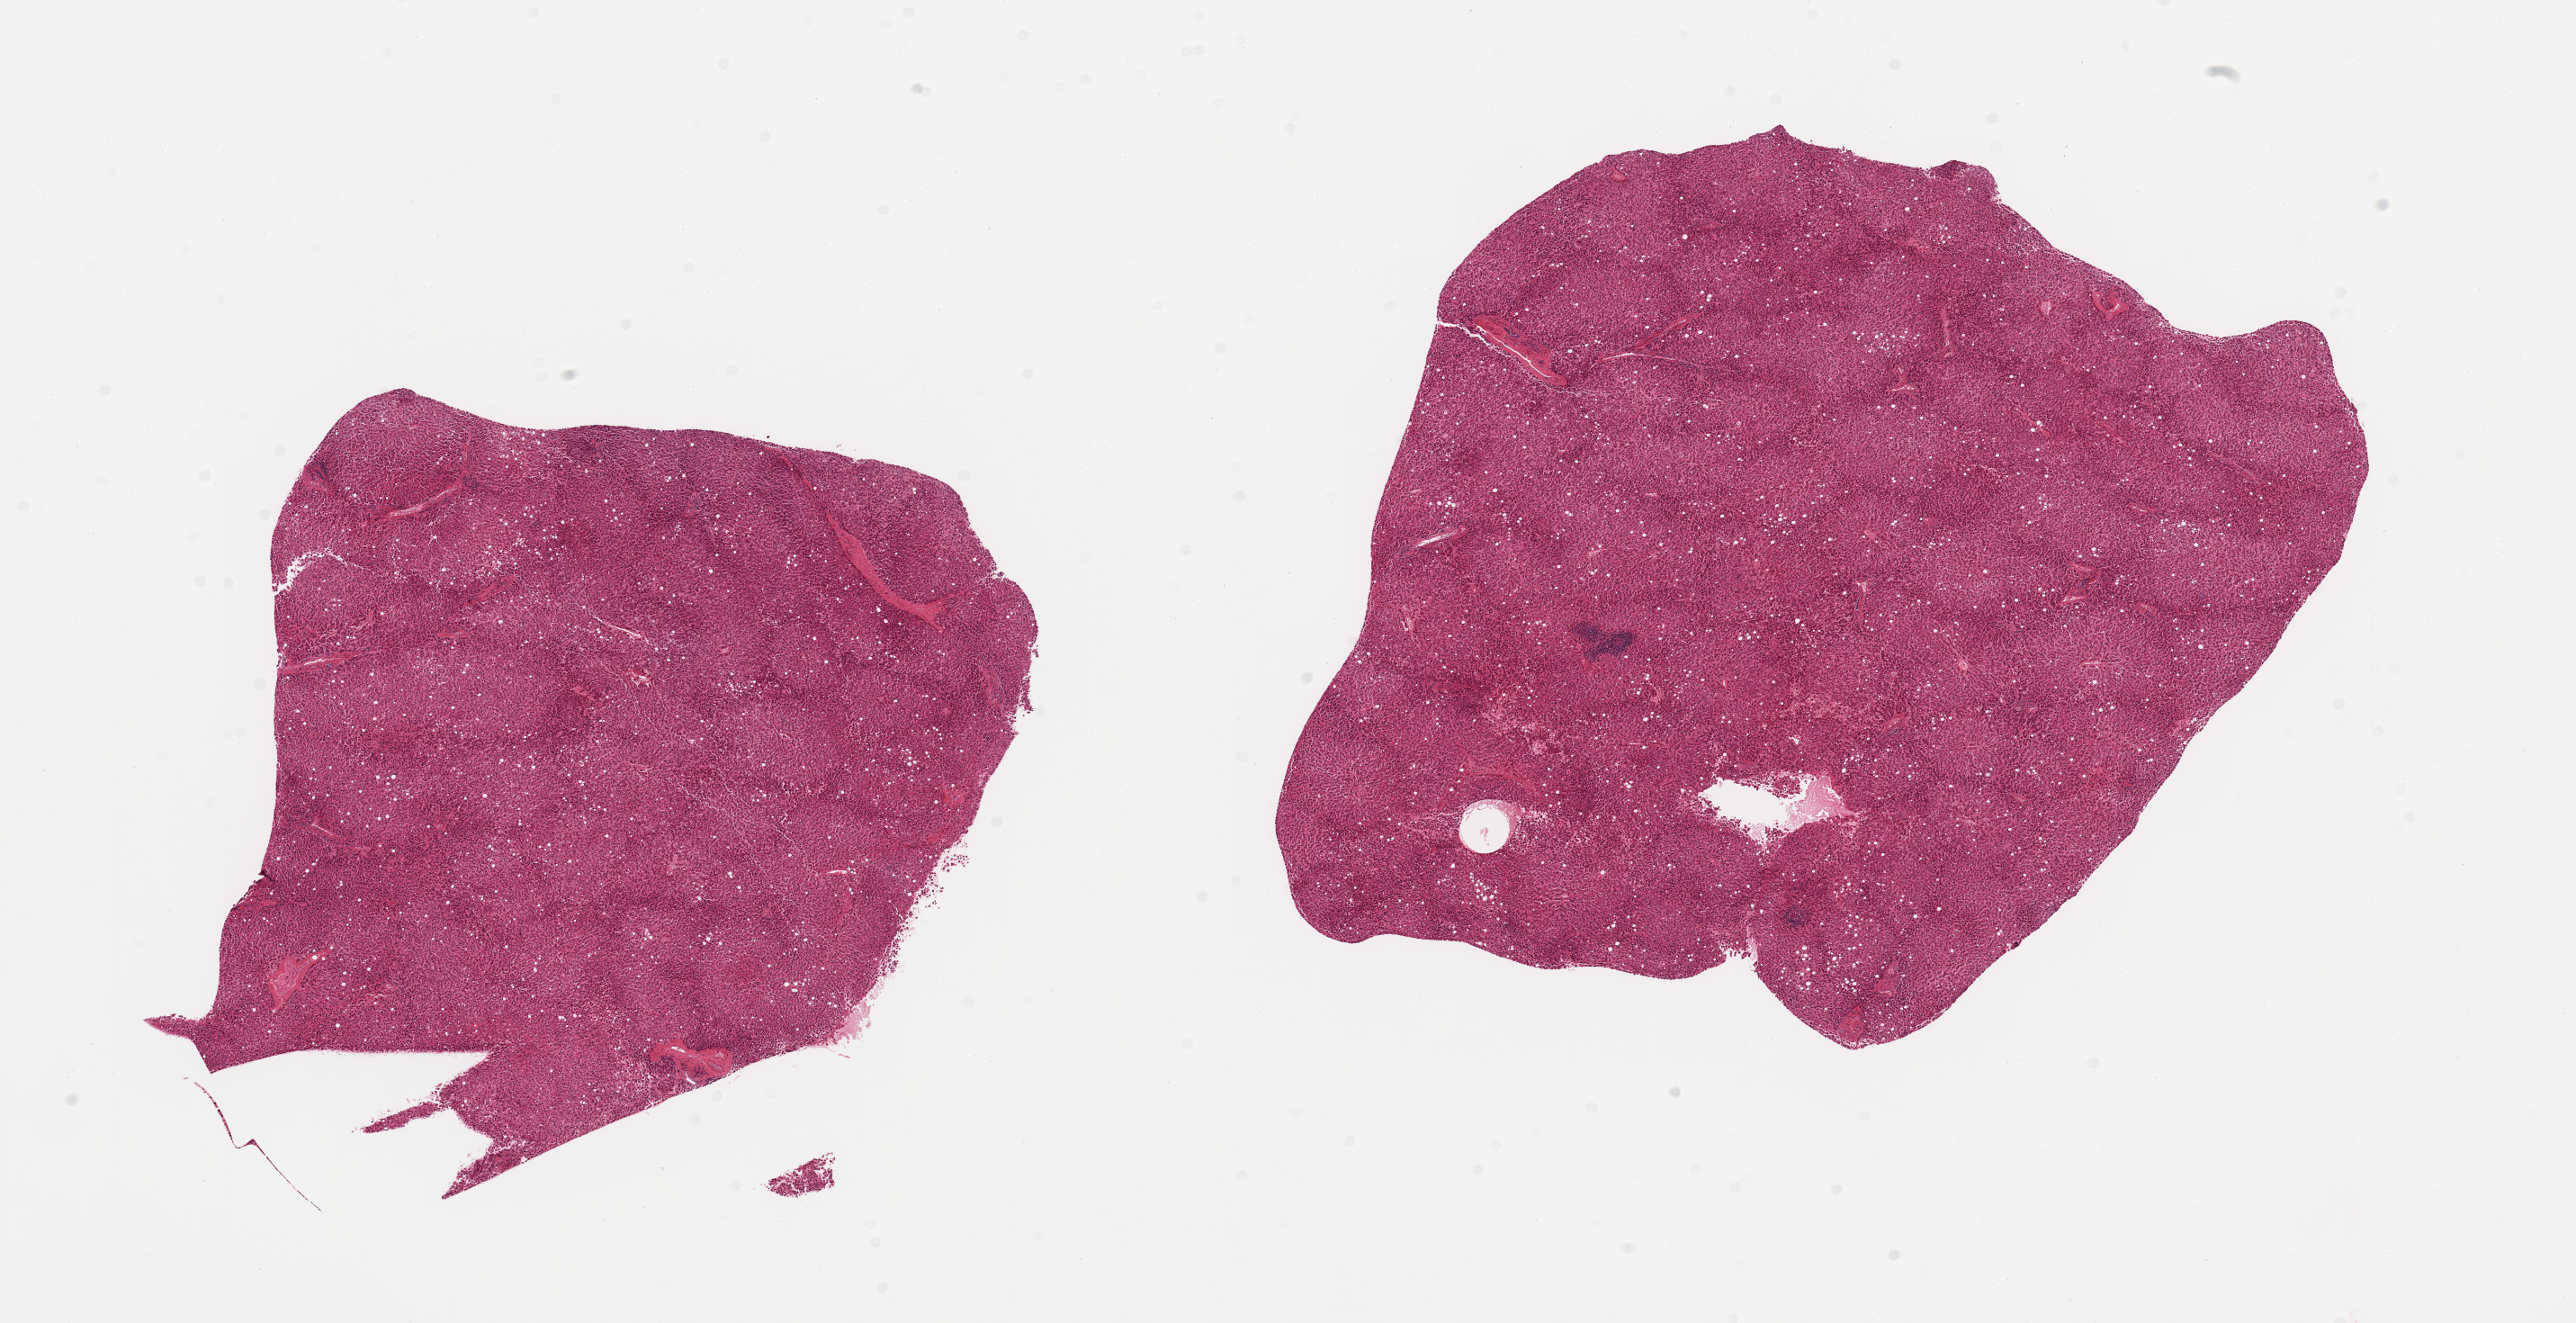
Haematoxylin and eosin whole-slide image — low-resolution overview of the scanned area, about 22.6 x 11.6 mm (acquisition: 20x scan). PAXgene-fixed, paraffin-embedded tissue. Target tissue: liver. Tissue donor sample. Donor sex: male.
Reviewer comment on this tissue sample: 2 pieces, ~5-10% steatosis, macro and microvesicular.